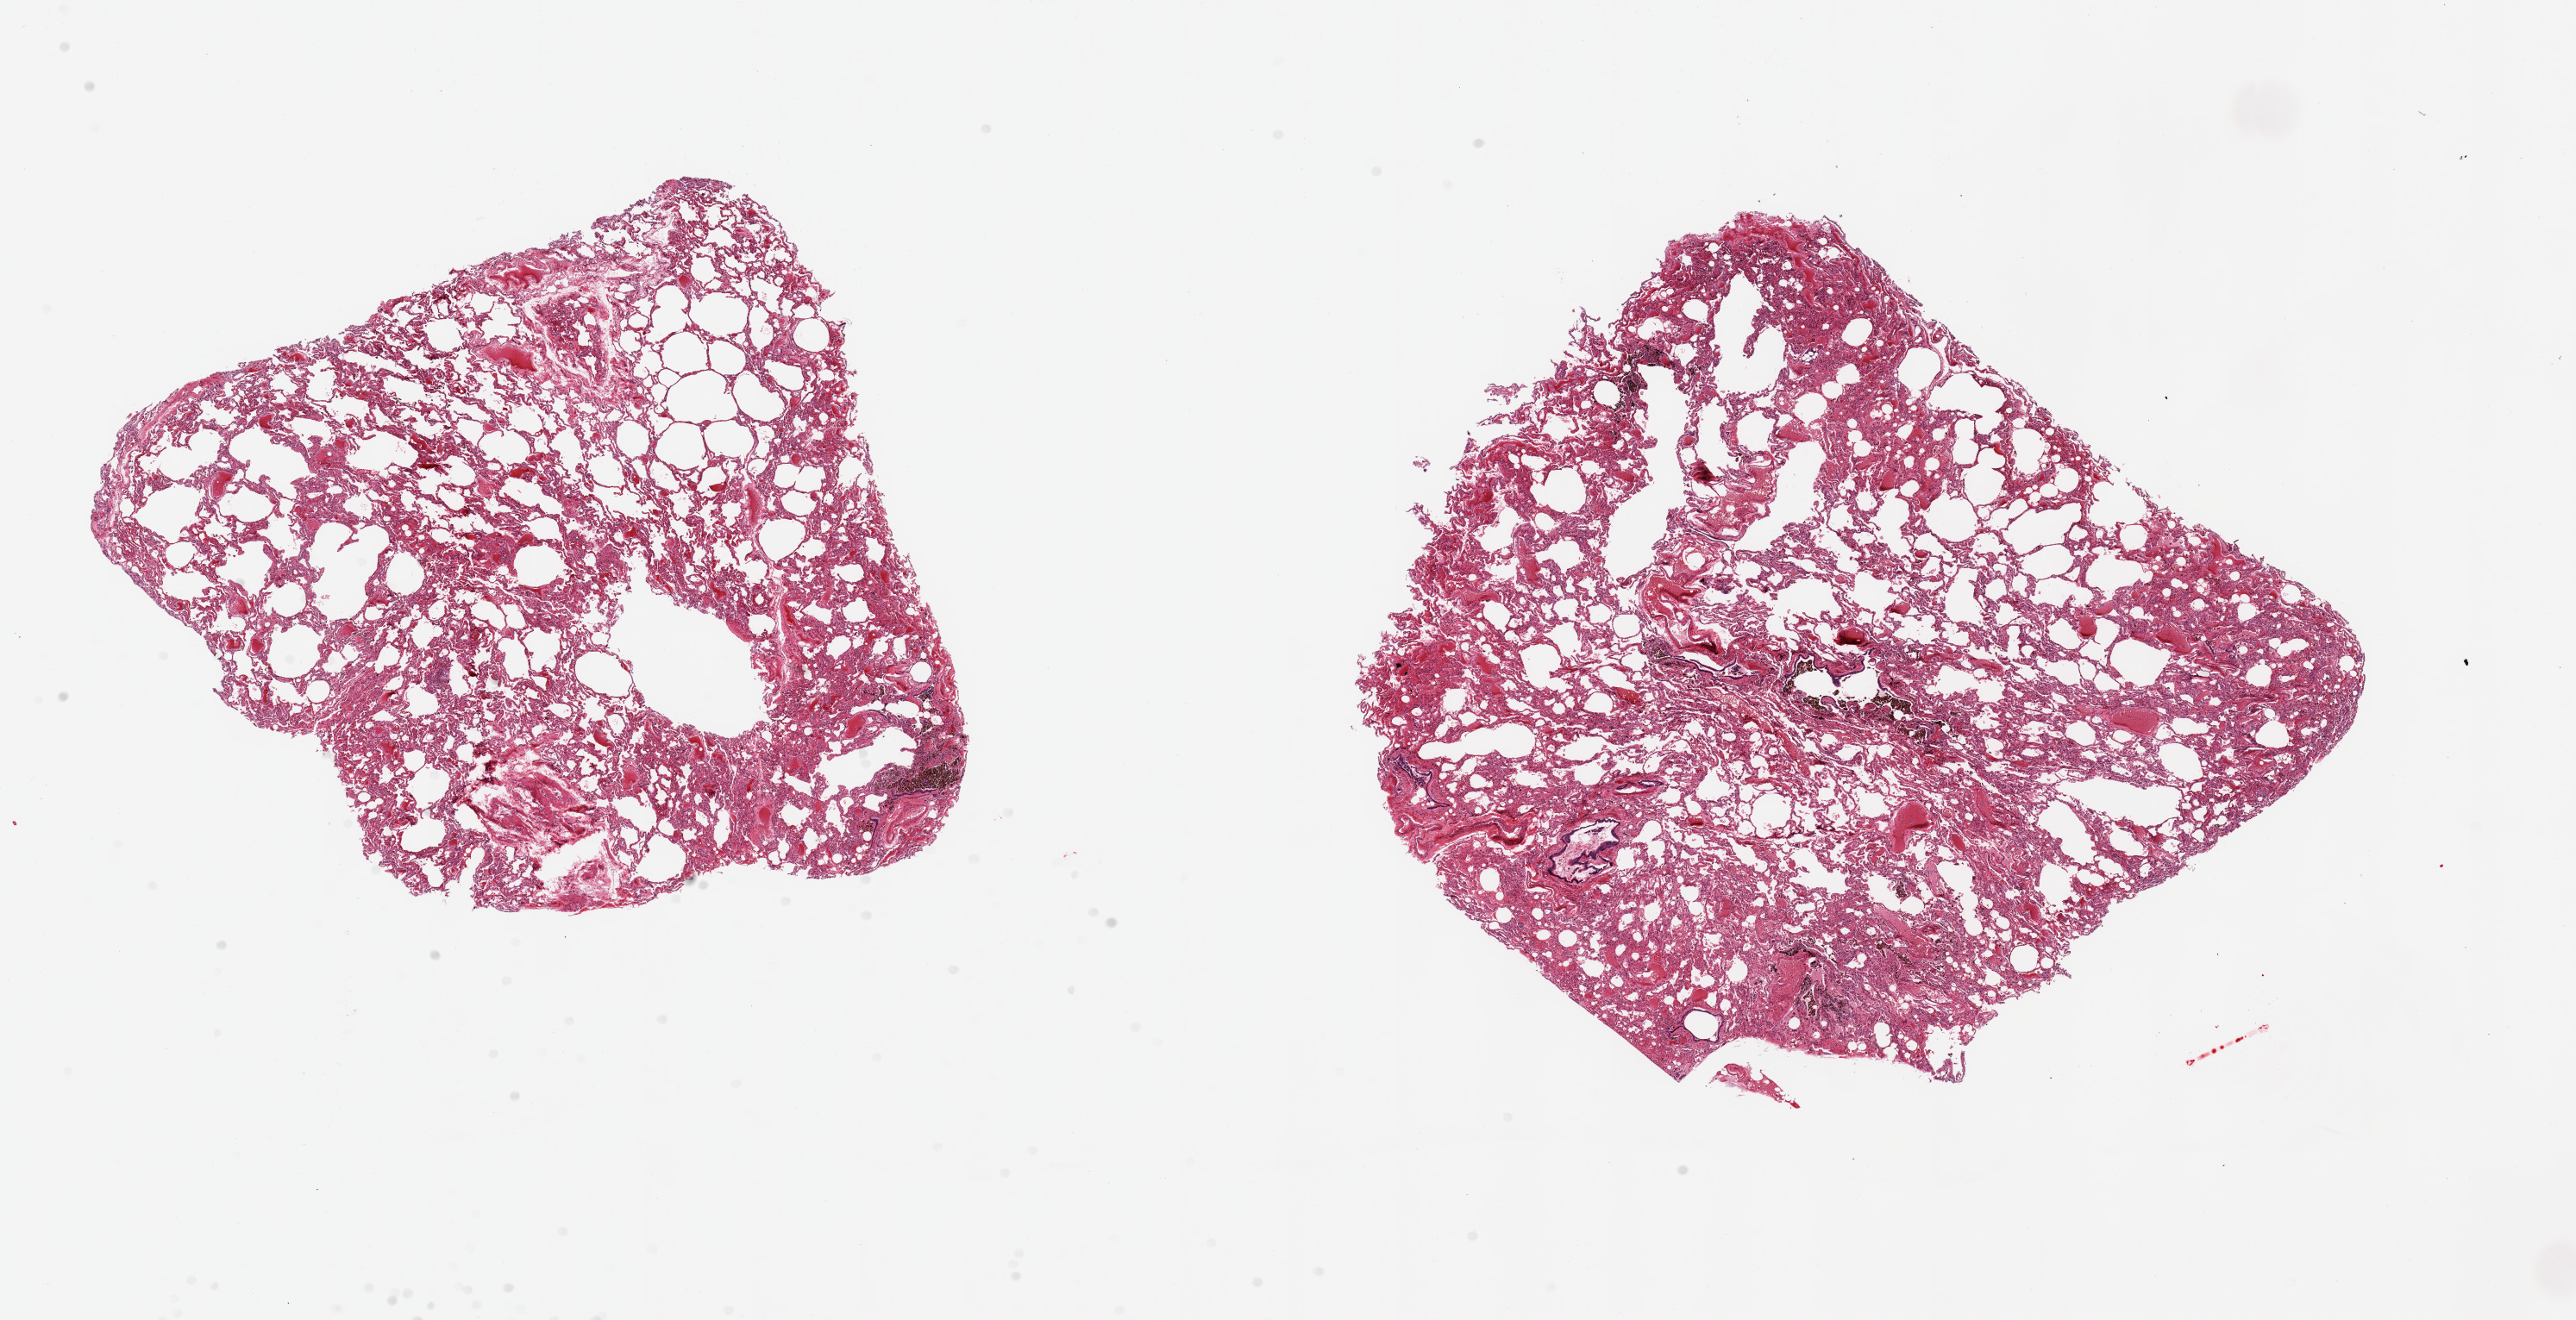
H&E whole-slide image — whole scanned area (about 23.6 x 12.1 mm) shown as a low-resolution overview. PAXgene-fixed, paraffin-embedded tissue. Target tissue: lung. Tissue donor sample. Donor sex: female.
Review note (as recorded): 2 pieces; emphysema; foci of pigmented macrophages.